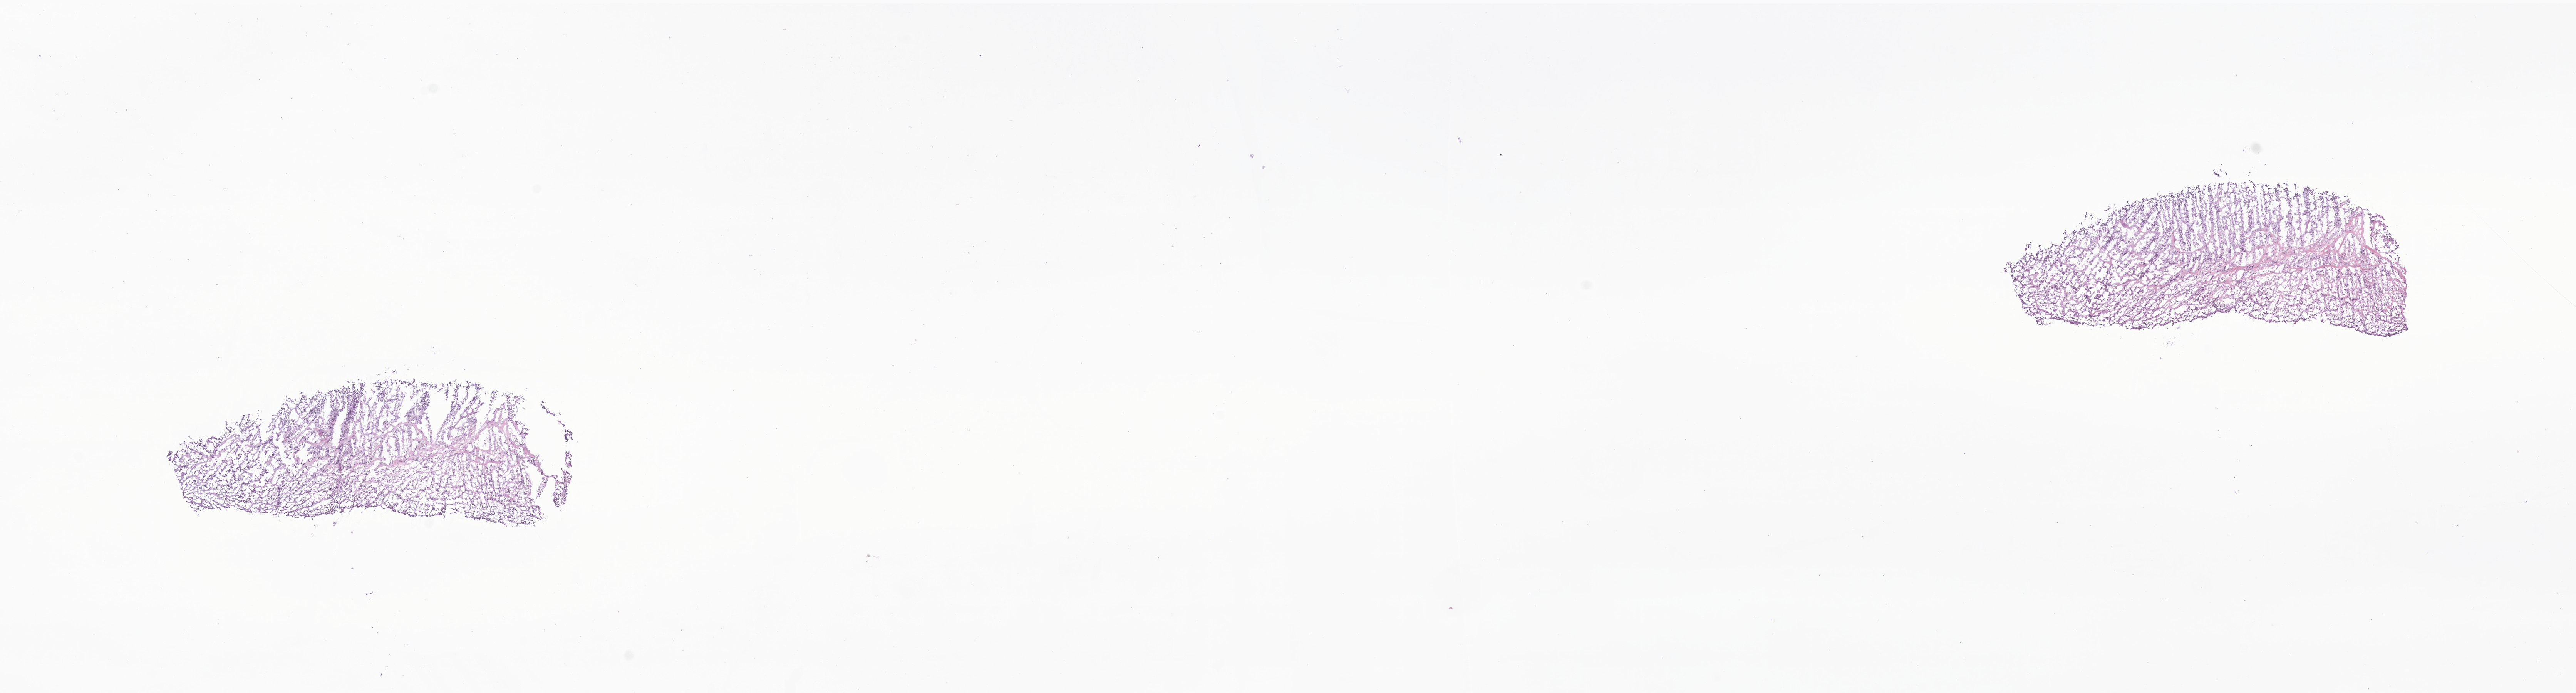
Hematoxylin and eosin (H&E) whole-slide image of tumor tissue from the tail of pancreas, shown as a low-resolution overview of the whole scanned area (about 28.2 x 7.6 mm). Frozen section. Patient: male, age 187 months (15 years 7 months).
Recorded diagnosis: Solid pseudopapillary neoplasm of pancreas.